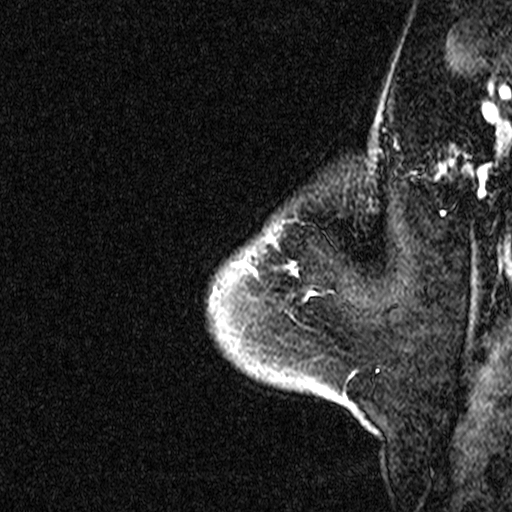
Breast MRI (dynamic contrast-enhanced), one sagittal slice; position 6 of 44 along the scan axis; dynamic contrast-enhanced study with each time point stored as its own series, time point 2 of 3 at this slice position (early post-contrast, ordered by acquisition time); 1.5 T; TE 4.5 ms, TR 11 ms; 512 × 512 image matrix, field of view 200 × 200 mm. Patient: female, 46 years. From the clinical record (not read from this slice): setting: breast cancer imaged before/during neoadjuvant chemotherapy; receptor status: HER2-positive.
Outlined on this slice (semi-automatically segmented with operator editing):
- analysis volume of interest (the breast-tissue region the enhancement analysis was run in; not a lesion): bounding box (x1, y1, x2, y2) in pixels: (224, 242, 359, 393)
- tumour enhancement mask (voxels above the 90 % enhancement threshold inside the analysis volume of interest): (293, 270, 297, 272)